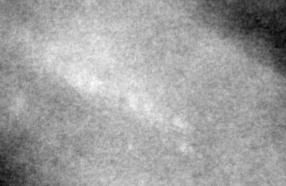
Cropped region of a digitized screen-film mammogram centred on a radiologist-marked abnormality; left breast; CC view.
Marked abnormality: calcifications, morphology pleomorphic, distribution linear; BI-RADS assessment category 4; subtlety rating 1 on a 1 (subtle) to 5 (obvious) scale; pathology result (as recorded, not read from the image): malignant.